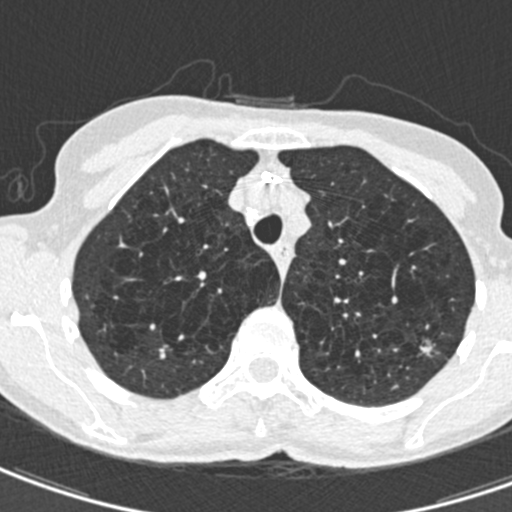
Axial slice from a low-dose chest CT screening exam; second annual screen; lung window (W 1500 / L -600 HU); 0.75 mm slice thickness; standard (soft-tissue) reconstruction kernel (B30f); 120 kVp; slice 120 of 498 in the series; 512 × 512 image matrix. Female participant, aged 71 years at enrolment.
Expert-annotated lung lesion, bounding box (x1, y1, x2, y2) in pixels: (404, 331, 444, 369). The screening reader recorded 2 non-calcified nodules or masses ≥4 mm on this exam (right upper lobe, left upper lobe); which of them this box marks is not recorded. Lung cancer was diagnosed 604 days after this screen: adenocarcinoma, NOS, left upper lobe, moderately differentiated (G2), stage IA (AJCC 6th edition), 12 mm at pathology.